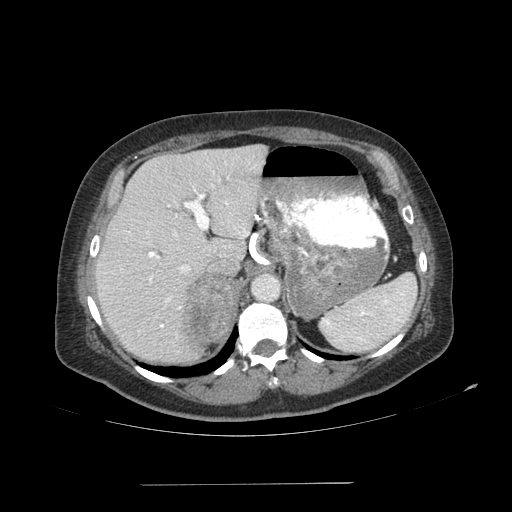
Contrast-enhanced abdominal CT, one axial slice; position 76 of 113 along the scan axis; 120 kVp; soft-tissue window (W 400 / L 40 HU); 2.5 mm slice thickness; 512 × 512 image matrix, field of view 440 × 440 mm. Patient: female, 67 years. Case-level facts recorded for this patient, not image findings: diagnosis: adrenocortical carcinoma; tumour side: right adrenal; tumour size at pathology: 9.8 cm; Ki-67 index: 59 %; stage (as recorded): 4.
Structures marked on this image (semi-automatic segmentation, software-assisted and operator-edited):
- mass: bounding box <184,276,237,341> (left, top, right, bottom; pixels)